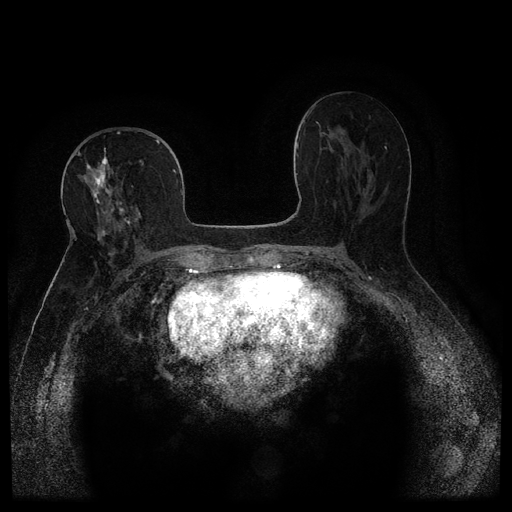
Breast MRI (dynamic contrast-enhanced, multi-phase), one axial slice; position 55 of 116 along the scan axis; dynamic contrast-enhanced series, time point 2 of 5 at this slice position (early post-contrast); 1.5 T; TE 2.6 ms, TR 5.4 ms; 2 mm slice thickness; 512 × 512 image matrix, field of view 340 × 340 mm. Female patient, age 68 years.
Outlined on this slice (semi-automatically segmented with operator editing):
- breast lesion (labelled 'tumour' in the annotation; benign lesions carry a separate 'benign' label): bounding box [x1, y1, x2, y2] px = [83, 149, 127, 223]